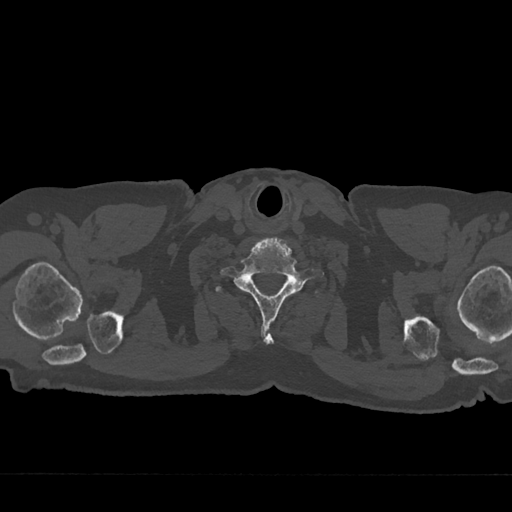
CT including the spine, one axial slice. Slice 690 of 797 in the series (ordered by position). Reconstruction kernel Br40s/3. Bone window (W 1800 / L 400 HU). 0.5 mm slice thickness. 512 × 512 image matrix. Male patient, age 75 years. Case-level facts recorded for this patient, not image findings: primary cancer: renal; vertebrae with lytic lesions (as recorded): T4.
Outlined on this slice (semi-automatic segmentation, software-assisted and operator-edited):
- T1 vertebra: bounding box <216,284,221,292> (left, top, right, bottom; pixels)